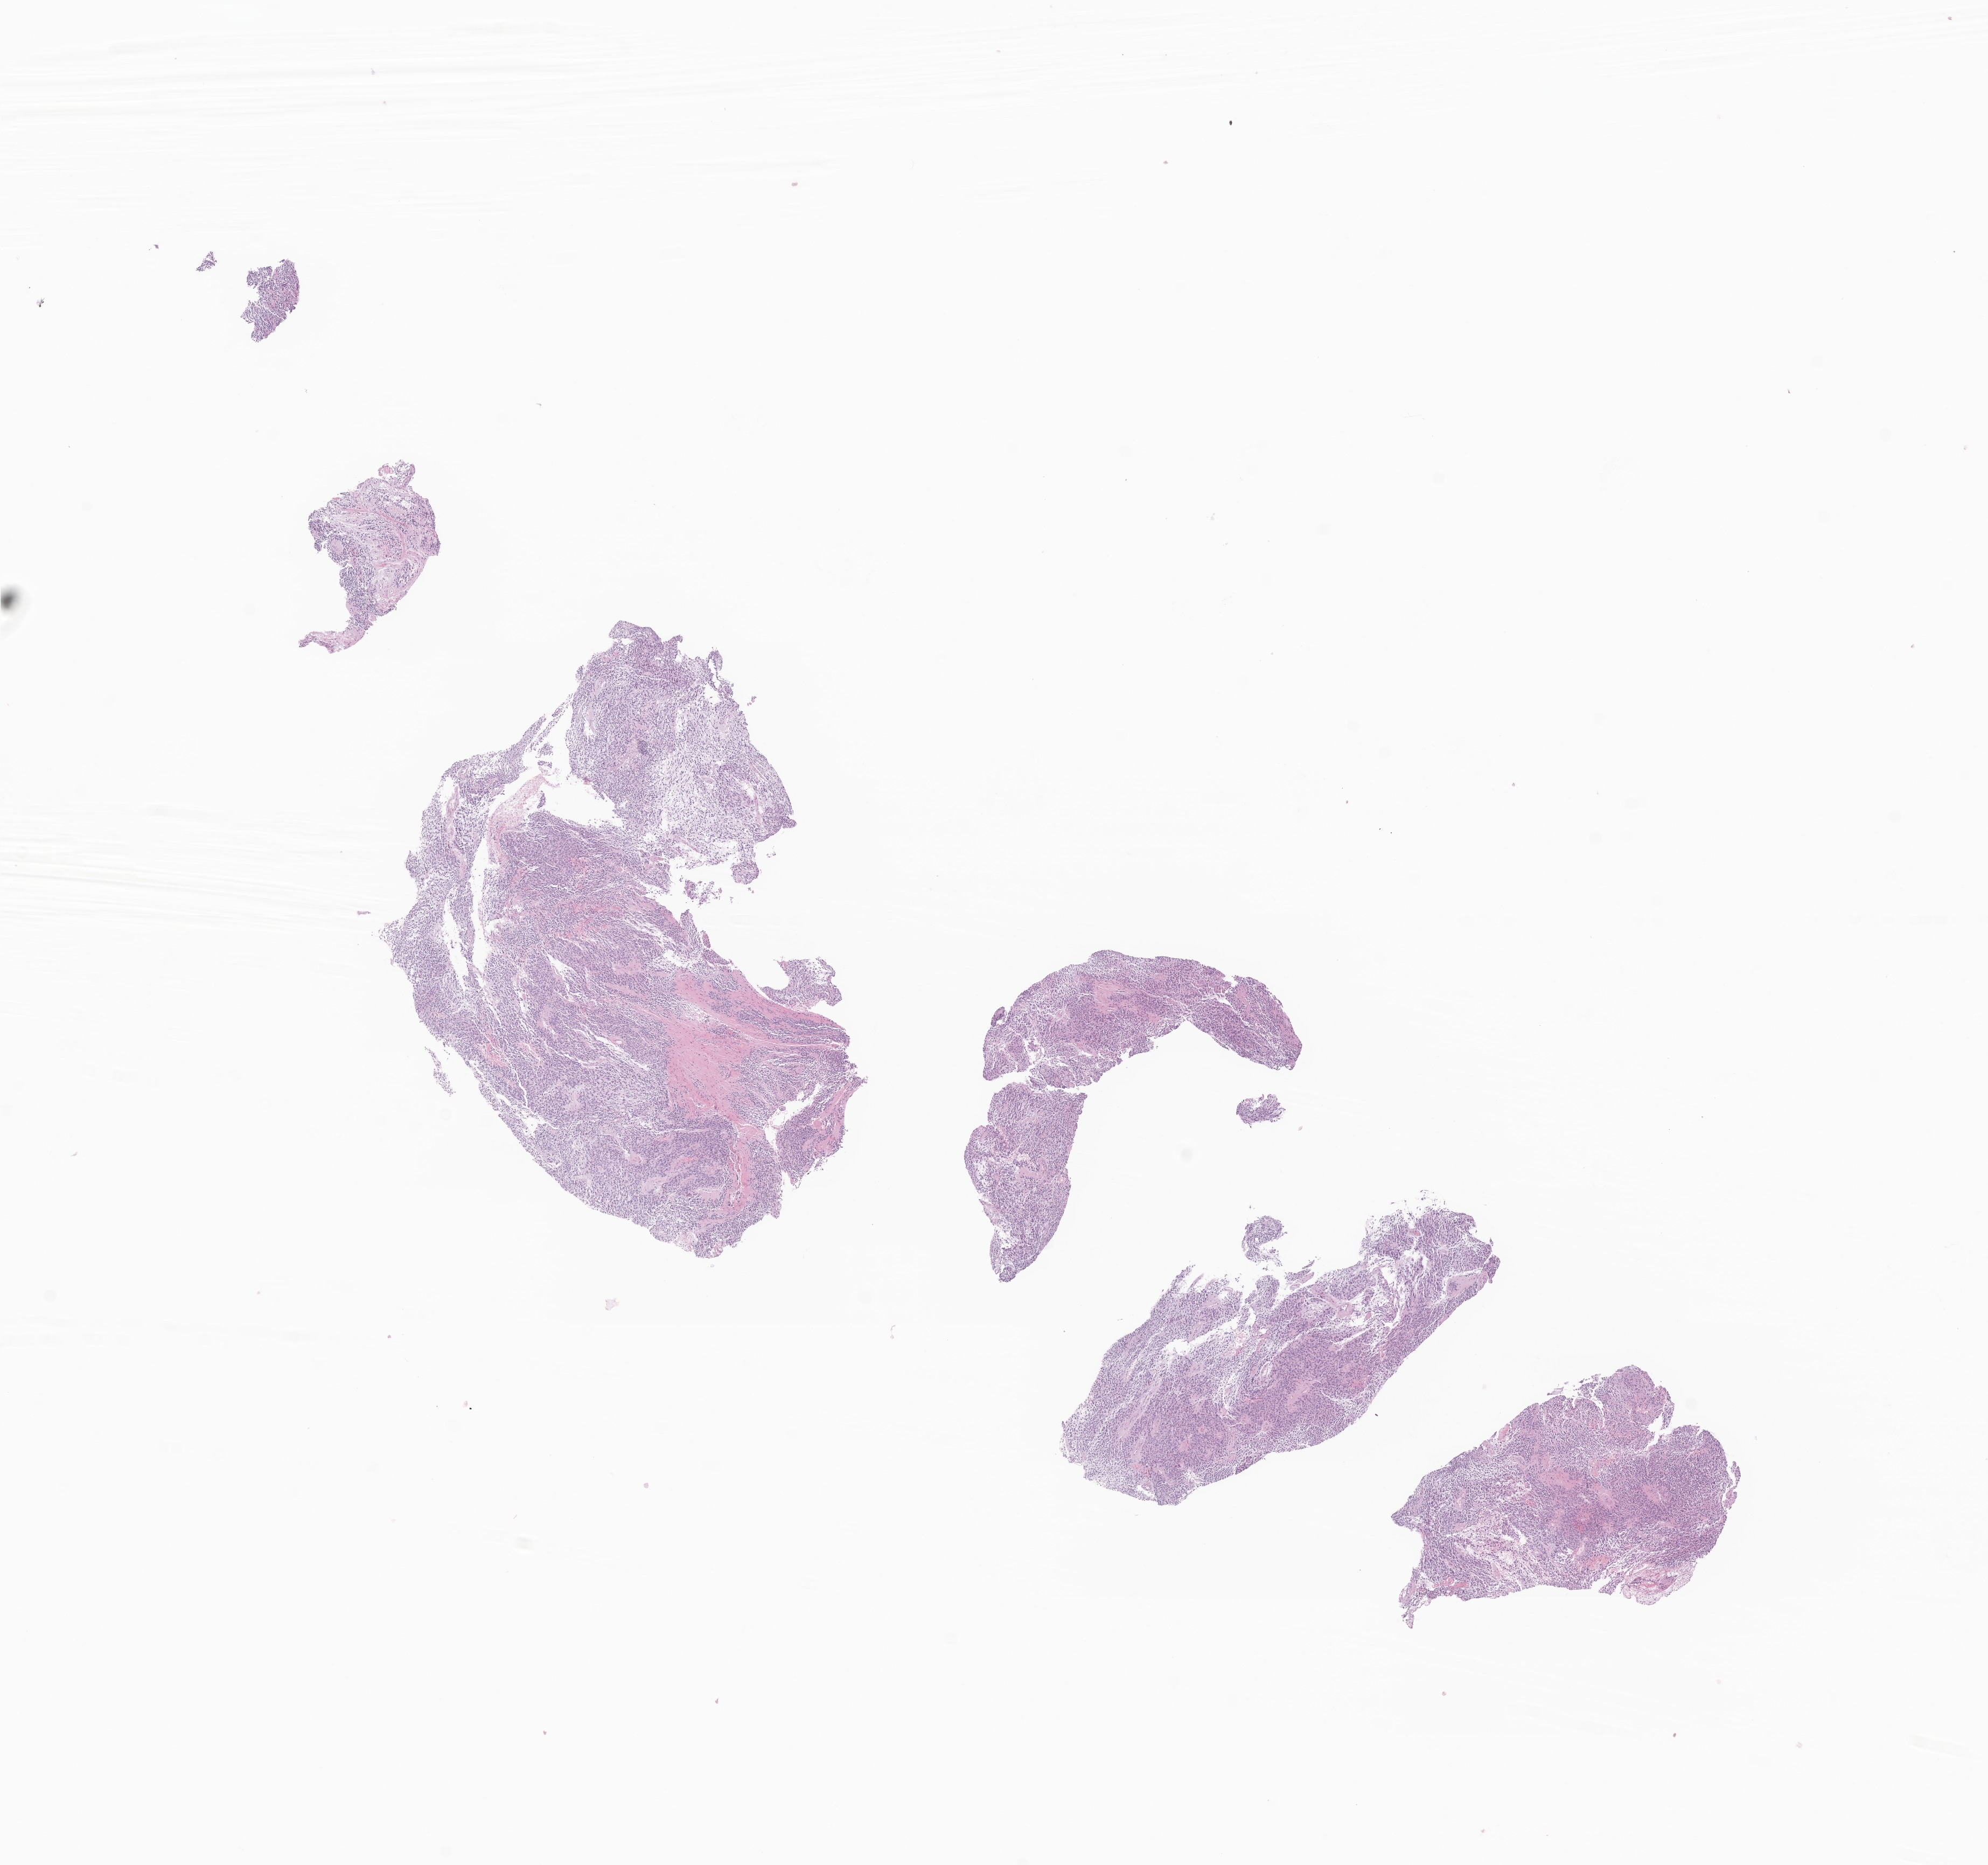
Whole-slide image, hematoxylin and eosin (H&E) stain of tumor tissue from the cerebral ventricle — low-resolution overview of the scanned area, about 15.6 x 14.6 mm. Formalin-fixed paraffin-embedded section. Patient: female, age 143 months (11 years 11 months).
Diagnosis (ICD-O-3 morphology term): Neoplasm, uncertain whether benign or malignant.